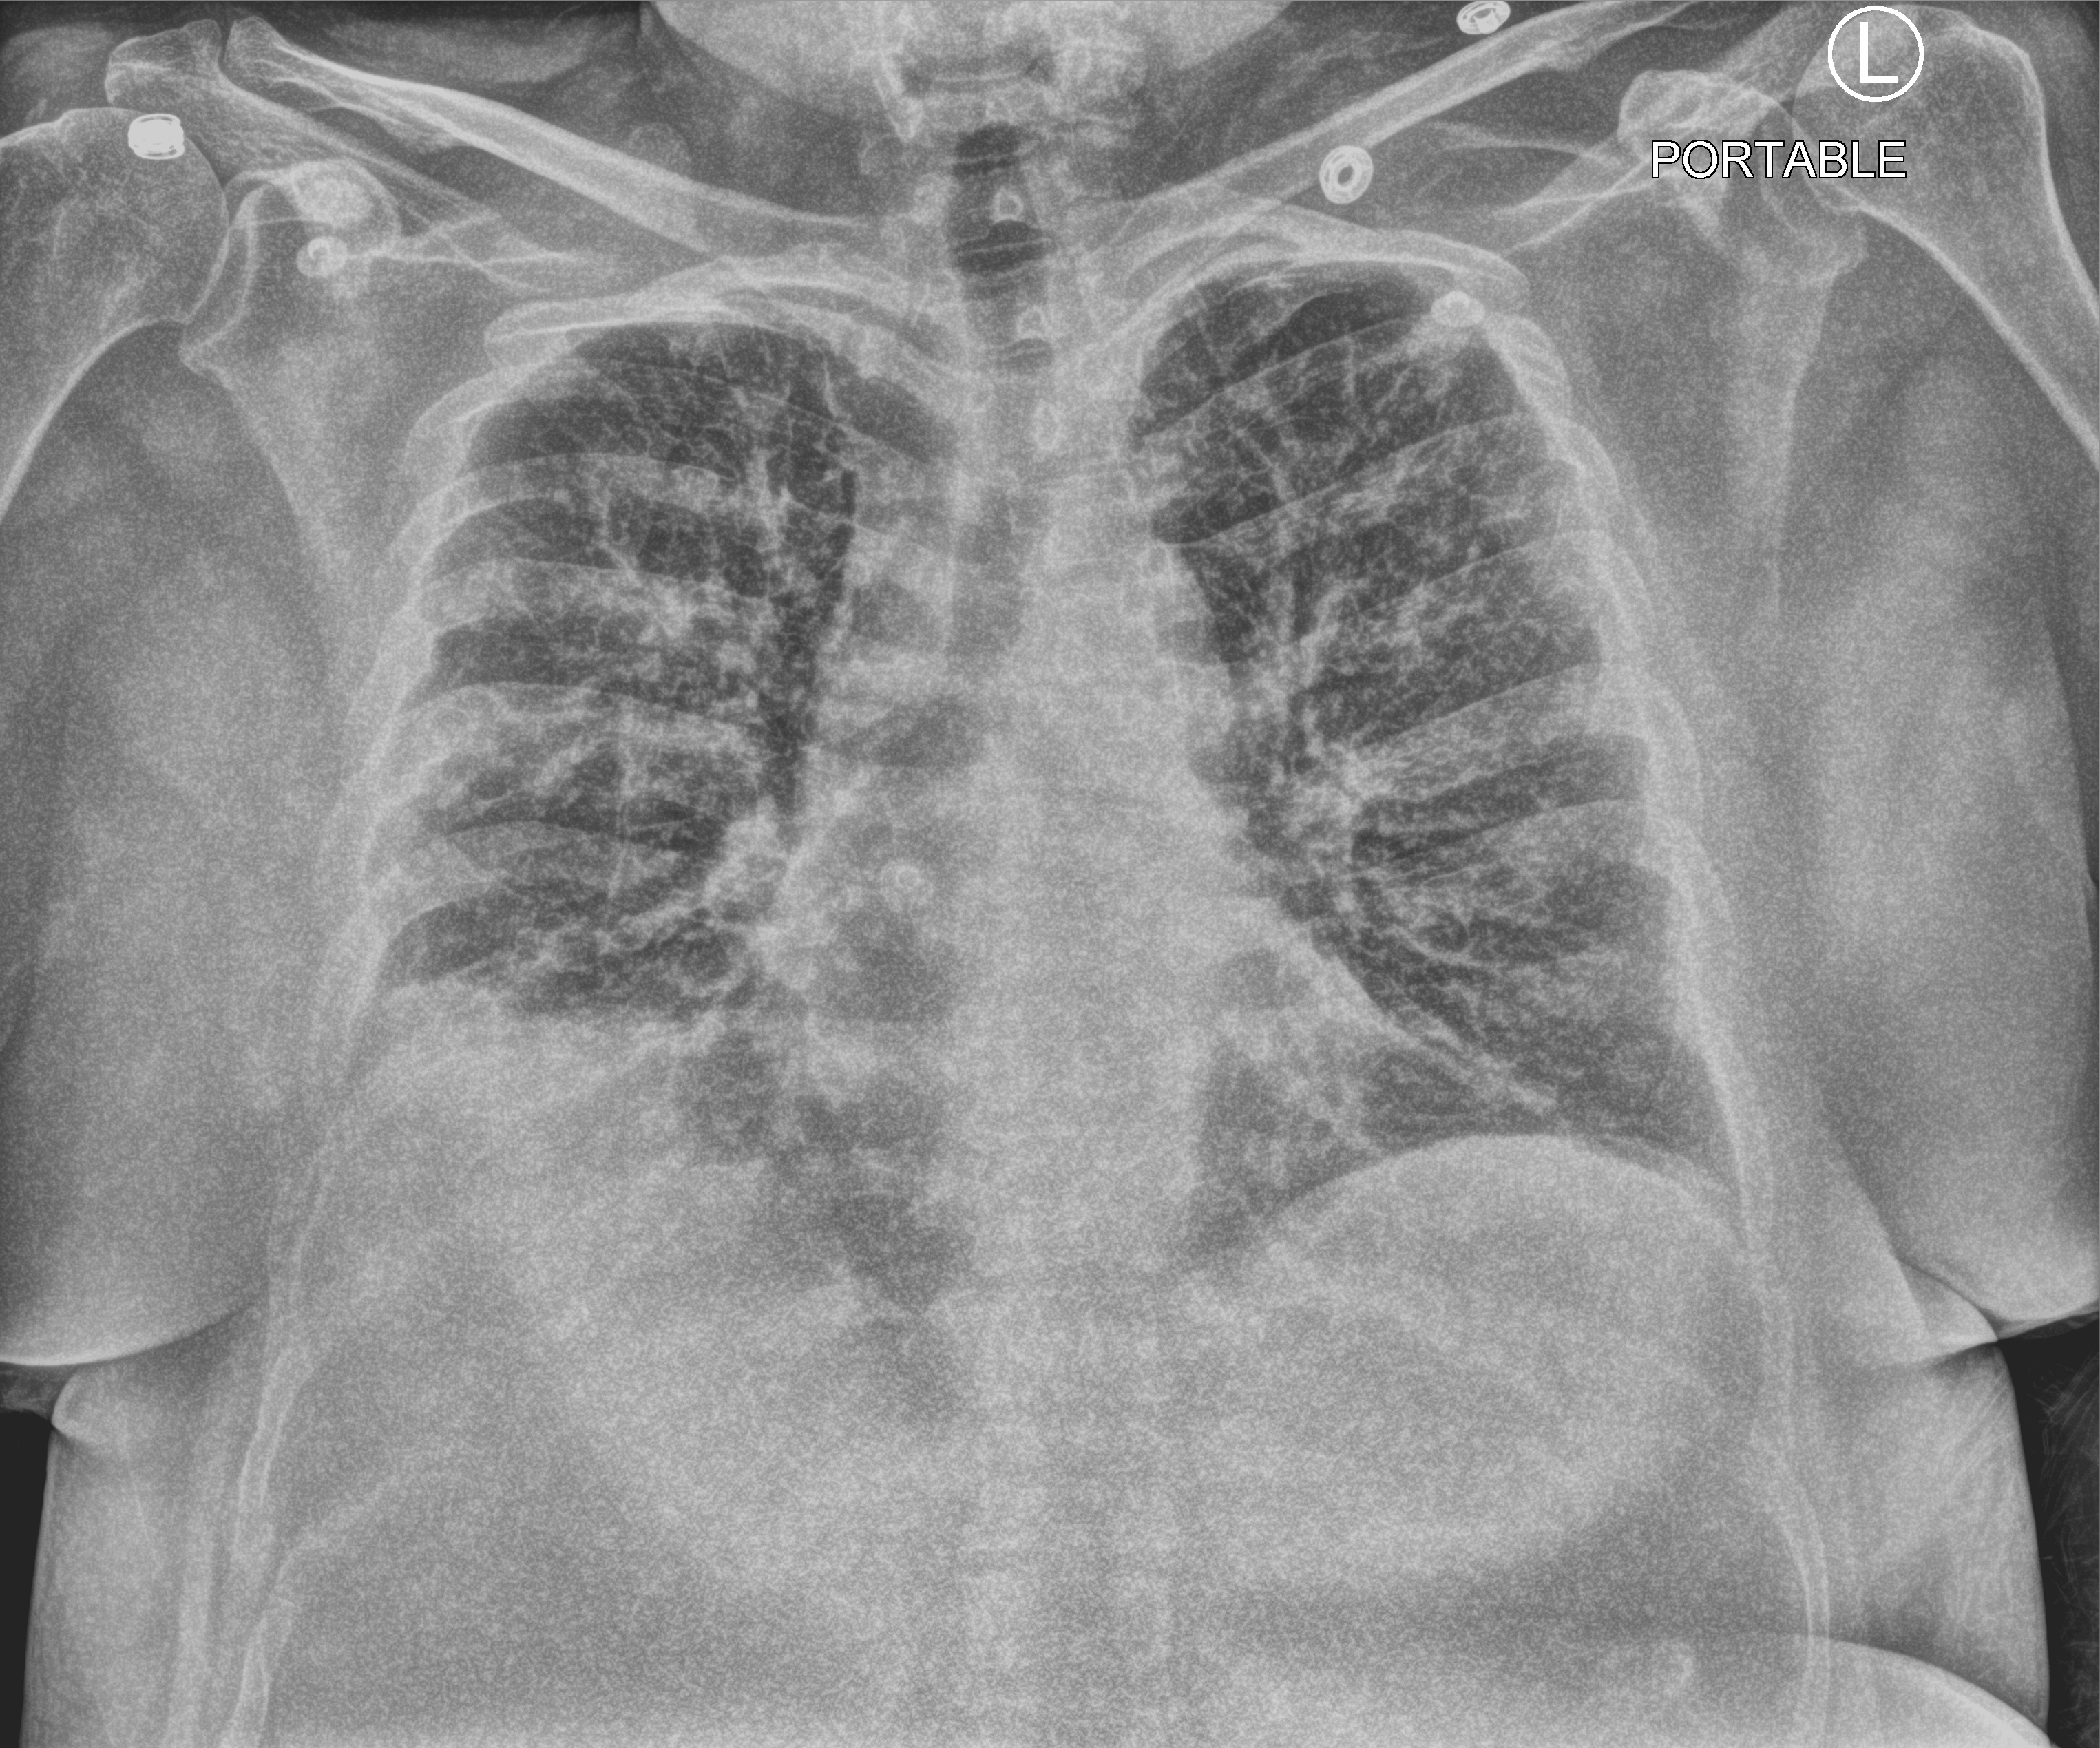
Bedside chest radiograph (computed radiography), anteroposterior (AP) projection. Patient hospitalised with COVID-19; female, aged 18–59 years.
From the hospital-stay record, not from the radiograph (when in the stay this image was taken is not recorded): admitted to intensive care during this hospital stay: no.